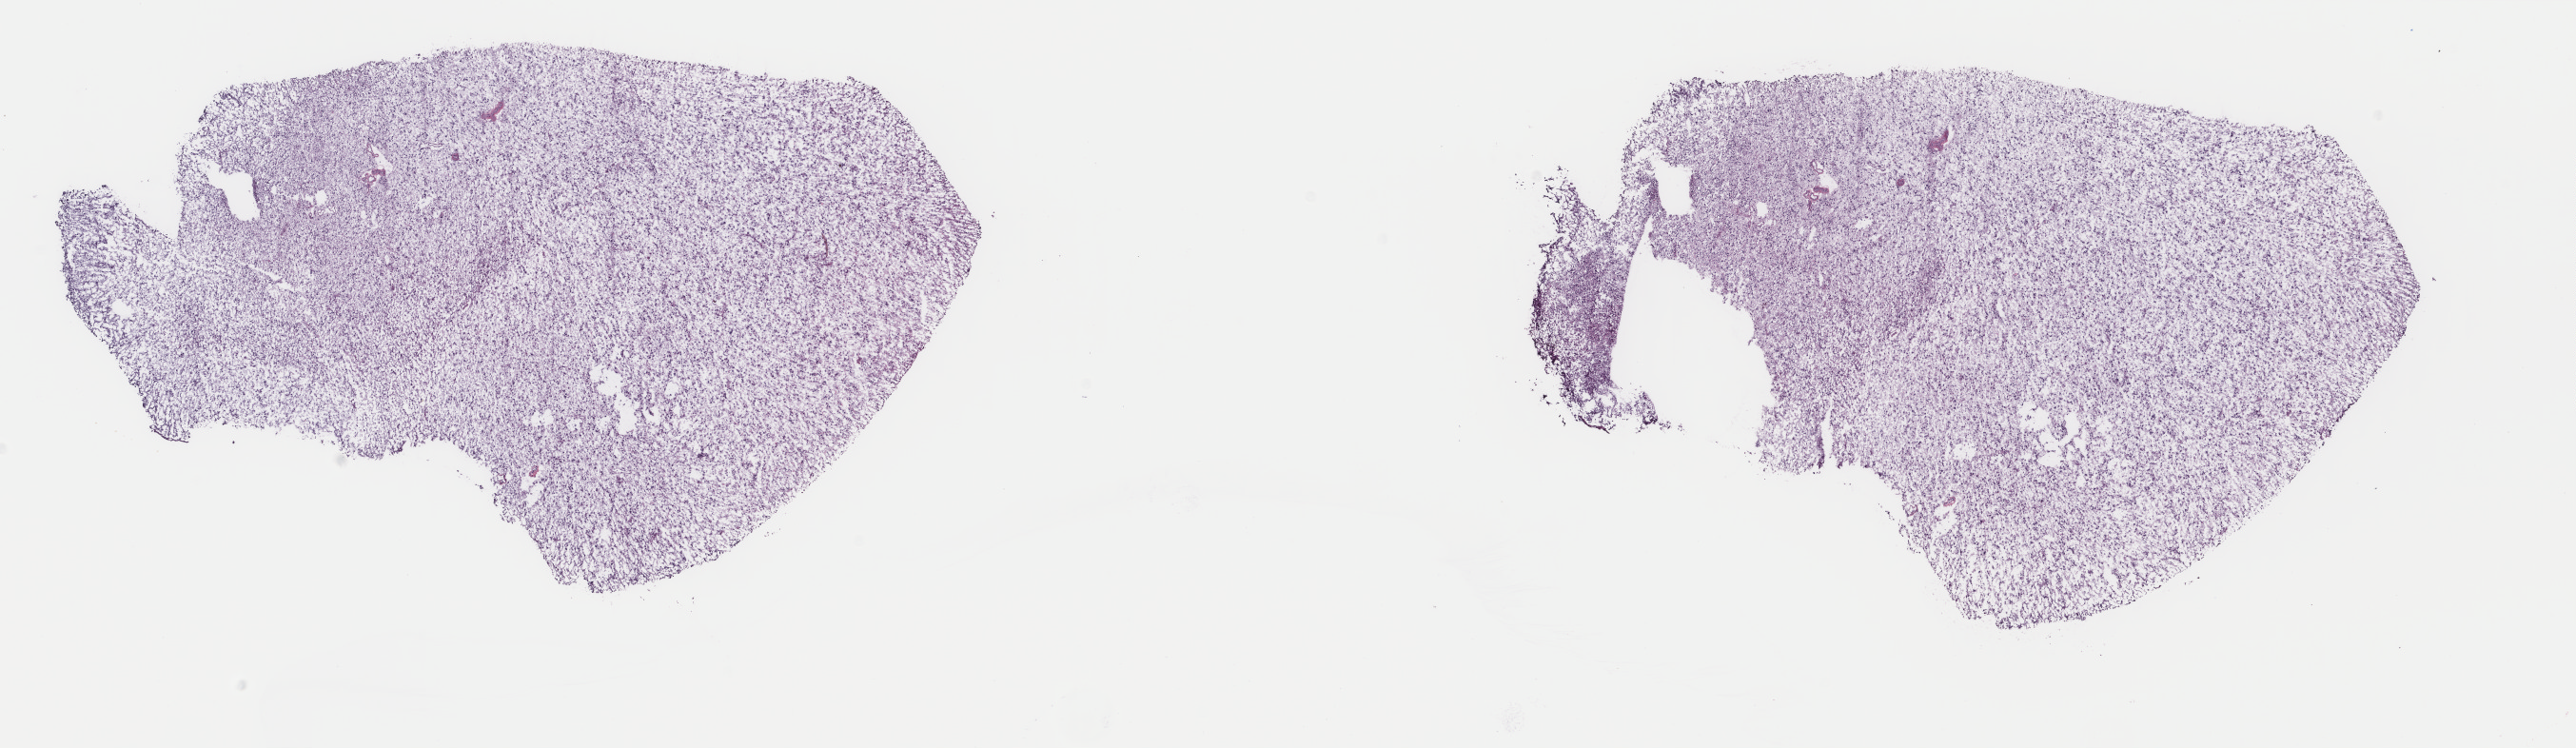
Whole-slide histology image, Hematoxylin and eosin (H&E) stained, shown as a low-resolution overview of the whole scanned area (about 21.5 x 6.2 mm, slide scanned at 40x), frozen section from the top of the tissue portion, sample: primary tumour, brain. Female patient; age at initial diagnosis 33 years. Histologic grade: G3 (poorly differentiated). Slide review estimates, as recorded: tumour cells 70%, tumour nuclei 80%, normal cells 10%, stromal cells 20%, necrosis 0%. Inflammatory infiltration, as recorded: lymphocyte infiltration 0%, monocyte infiltration 0%, neutrophil infiltration 0%.
Pathologic diagnosis: Astrocytoma, anaplastic.